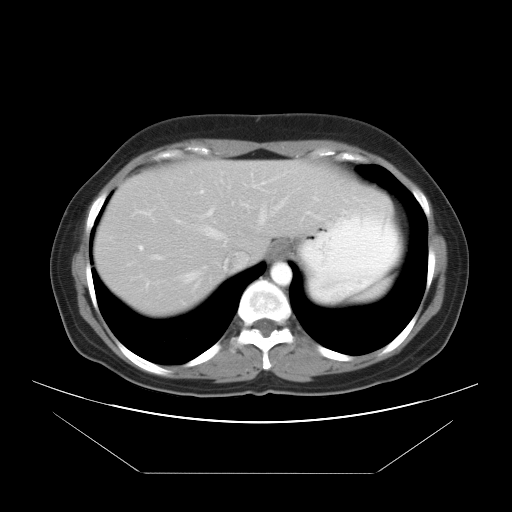
Contrast-enhanced abdominal CT, one axial slice. Position 30 of 34 along the scan axis. Intravenous contrast given. Soft-tissue window (W 400 / L 40 HU). 512 × 512 image matrix. Female patient, age 38 years. Case-level facts recorded for this patient, not image findings: diagnosis: colorectal cancer liver metastases, imaged before liver resection; multiple liver metastases: yes; largest metastasis: 3.1 cm.
Annotated regions visible in this slice (expert manual segmentation):
- hepatic veins: bounding box [x1, y1, x2, y2] px = [178, 201, 284, 284]
- liver: [94, 160, 364, 316]
- planned liver remnant (the part of the liver to remain after resection): [200, 160, 365, 261]
- portal vein (with intrahepatic branches): [140, 186, 268, 249]